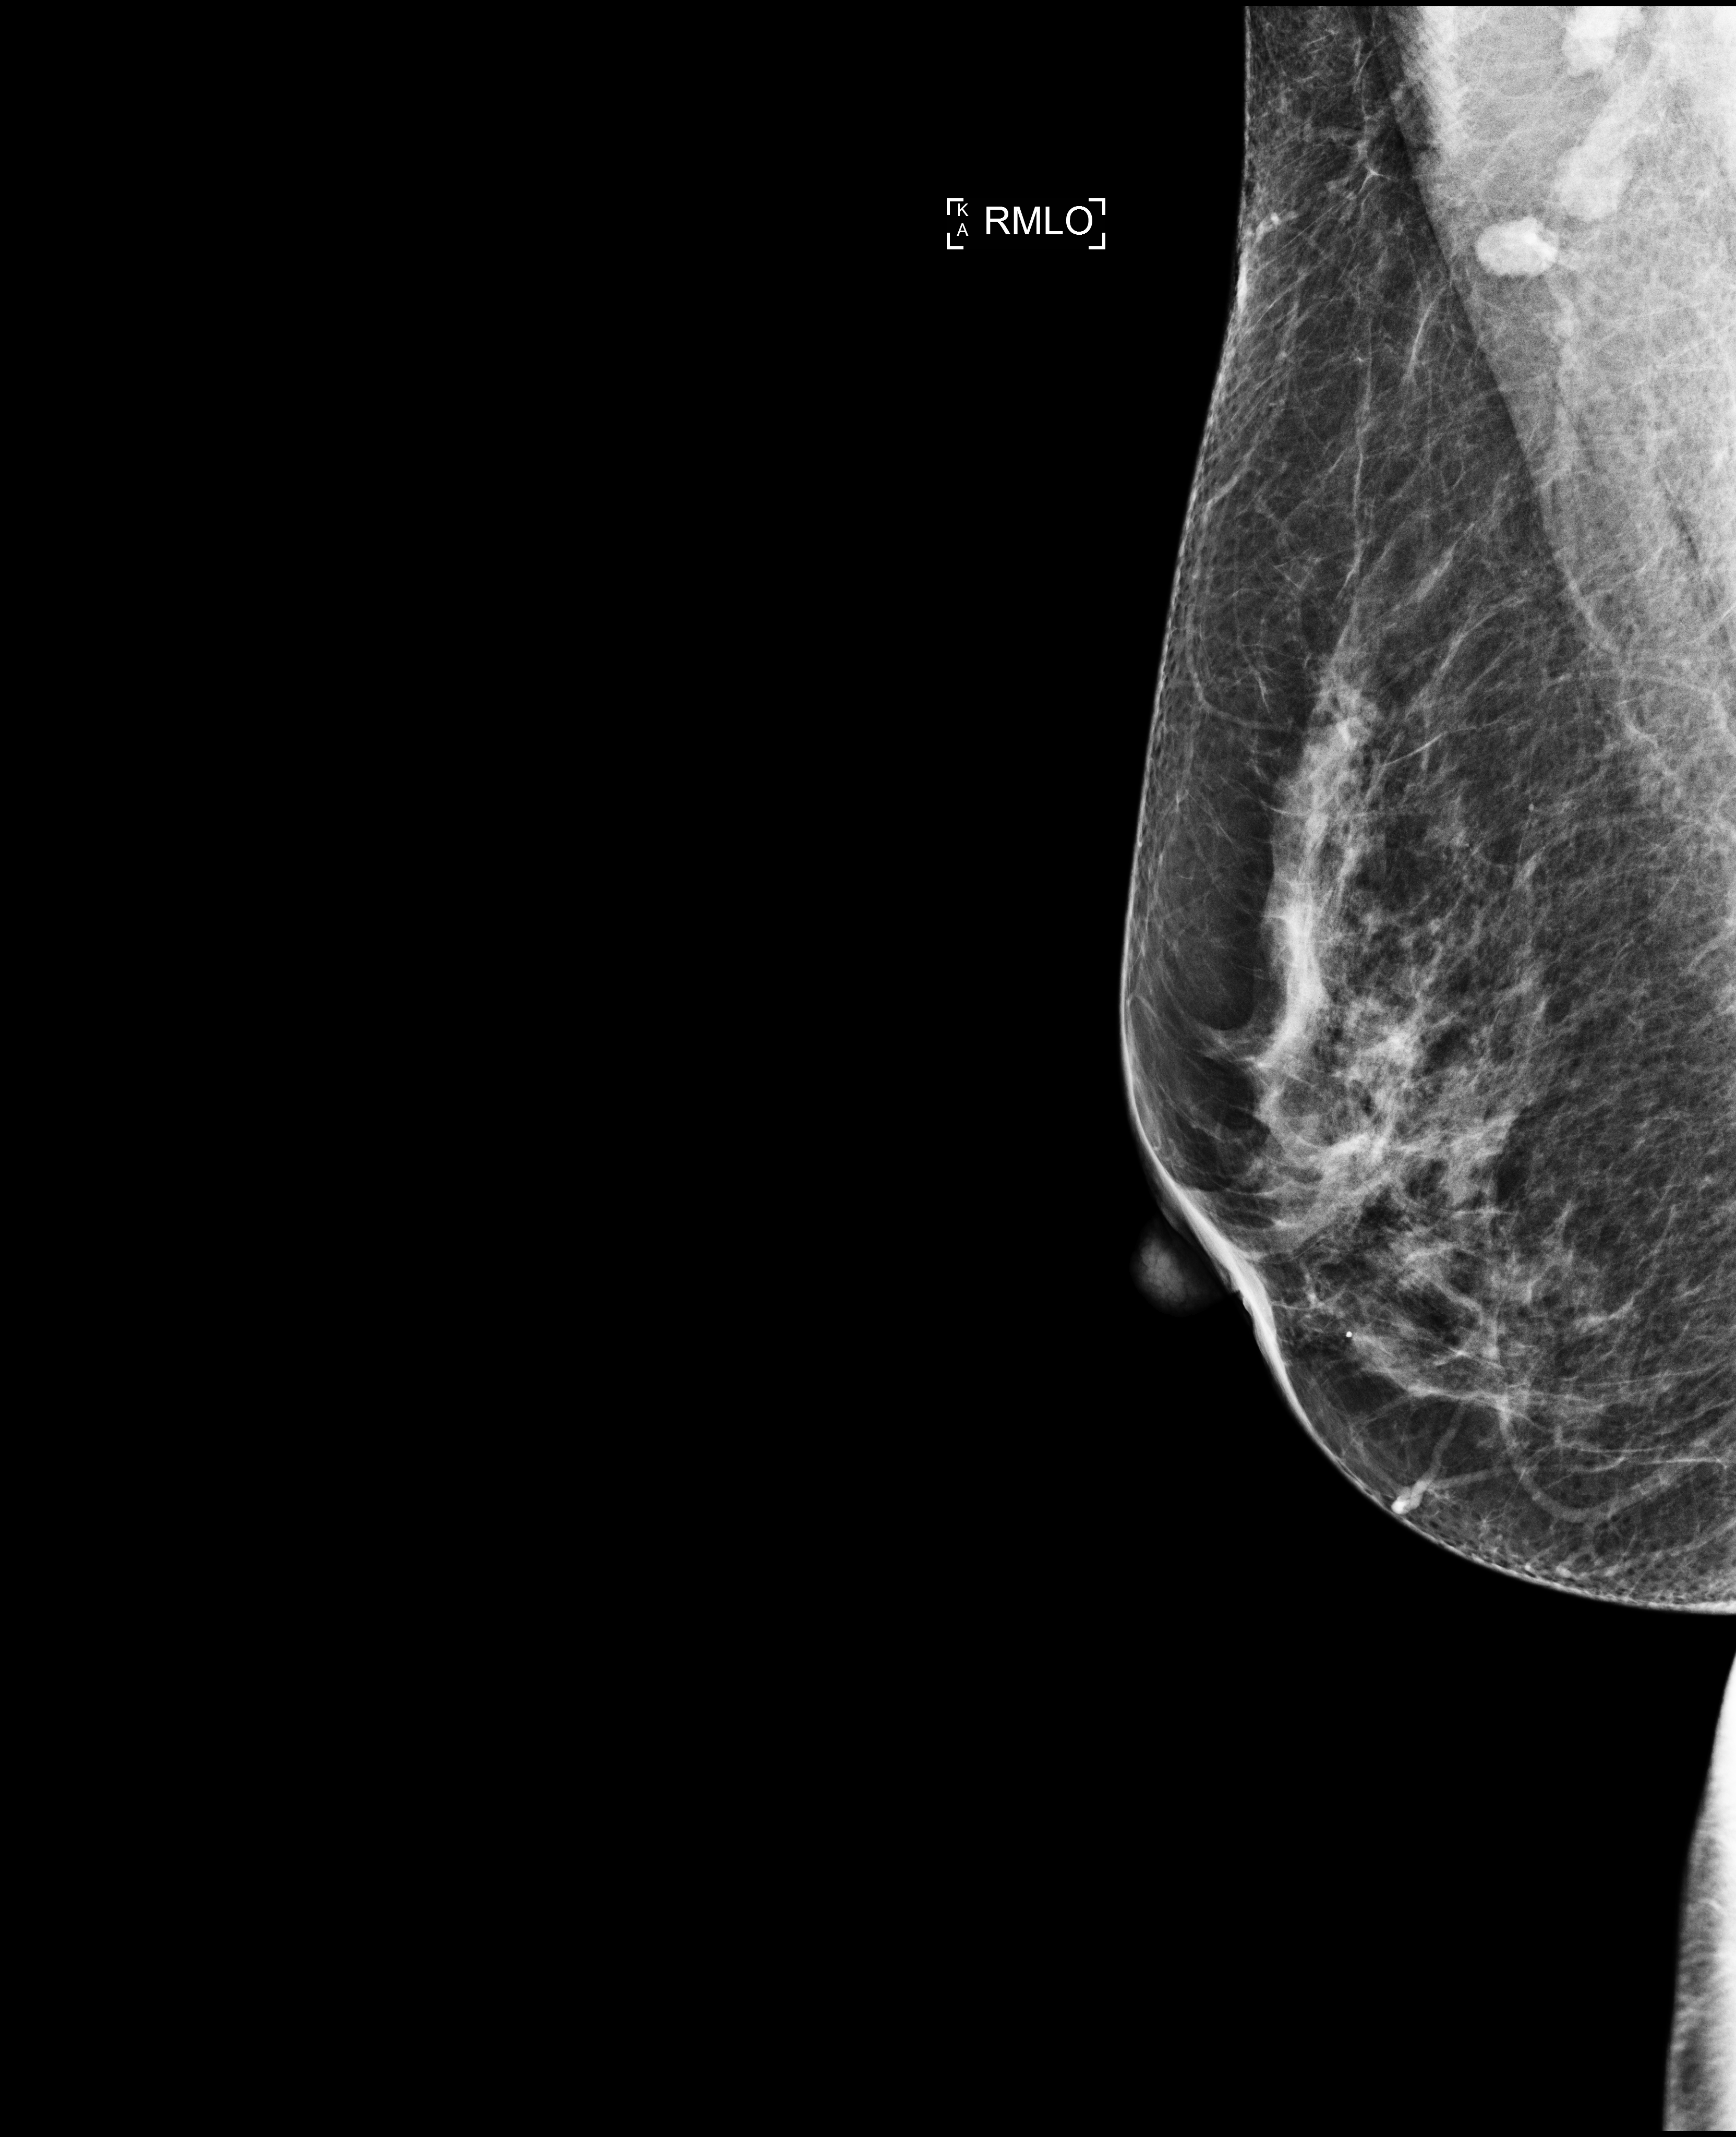
Screening examination, compressed breast thickness 56 mm, system: Selenia Dimensions. Patient: female, 52 years.
Image type: full-field digital mammogram. Breast: right. Projection: medio-lateral oblique projection.